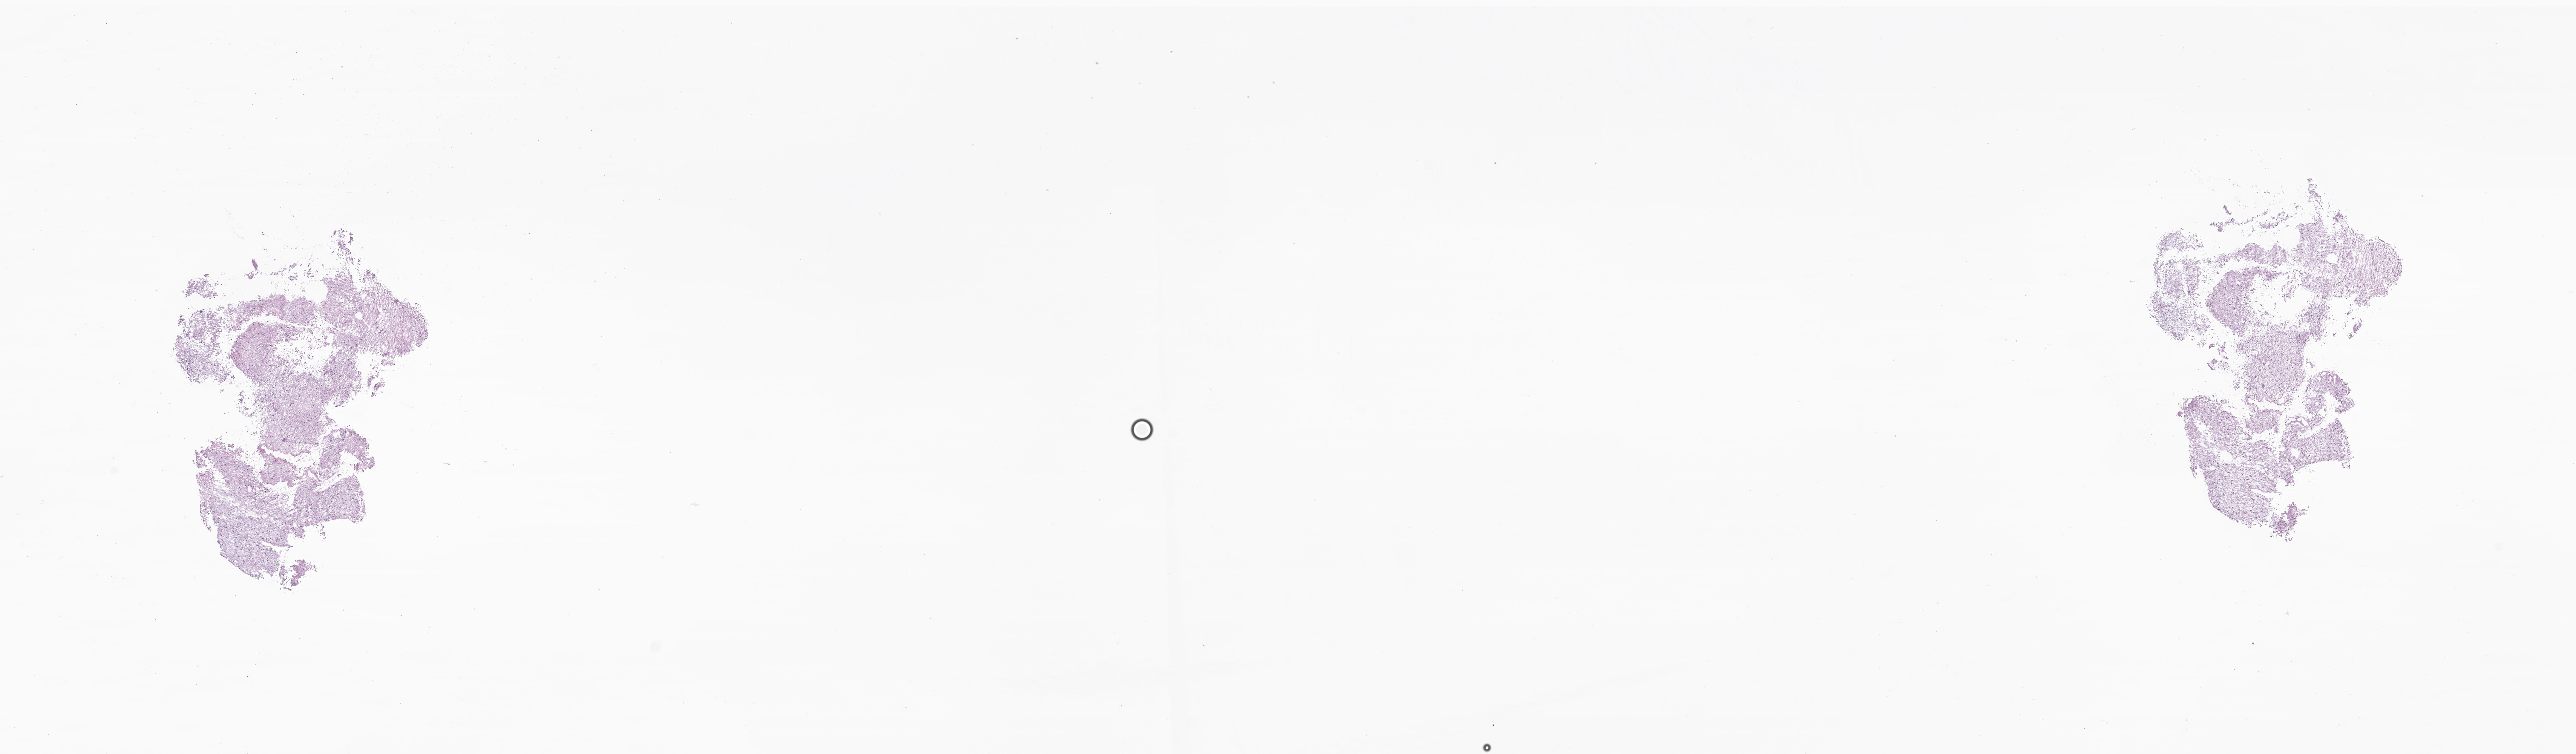
Digitized H&E-stained section of tumor tissue from the cerebellum, whole scanned area (about 28.8 x 8.4 mm) shown as a low-resolution overview. Frozen section. Male patient, age 190 months.
Diagnosis (ICD-O-3 morphology term): Pilocytic astrocytoma.